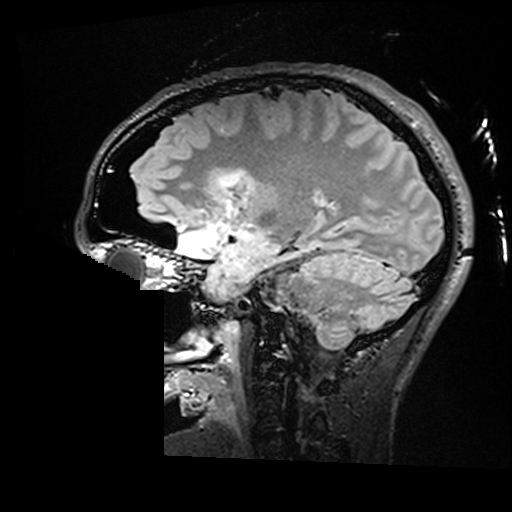
Brain MRI from a brain-tumour surgery series, one sagittal slice; slice 104 of 176 in the series (ordered by position); T2 FLAIR; 1 mm slice thickness; 512 × 512 image matrix. Case-level facts recorded for this patient, not image findings: histopathology: Astrocytoma; WHO grade: 2; IDH mutation: yes; tumour location: Right Insular.
Structures marked on this image (outlined manually by an expert reader):
- residual tumour: bounding box [x1, y1, x2, y2] px = [217, 170, 245, 188]